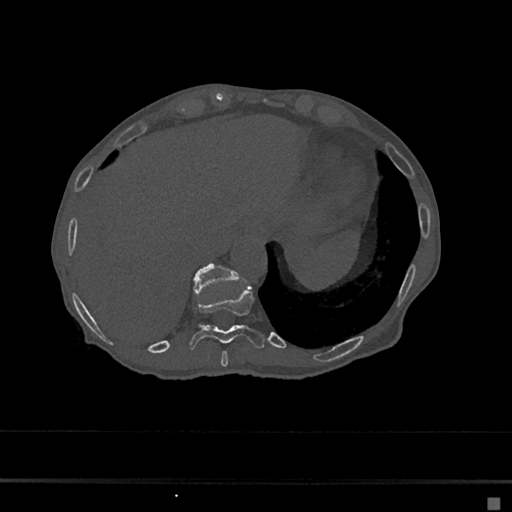
CT including the spine, one axial slice; reconstruction kernel Br40s/3; 120 kVp; bone window (W 1800 / L 400 HU); 0.5 mm slice thickness; 512 × 512 image matrix, field of view 360 × 360 mm. Patient: female, 68 years. From the clinical record (not read from this slice): primary cancer: renal.
Structures marked on this image (semi-automatically segmented with operator editing):
- T10 vertebra: bounding box [x1, y1, x2, y2] px = [188, 286, 265, 350]
- T11 vertebra: [193, 263, 239, 295]
- T9 vertebra: [220, 351, 228, 367]